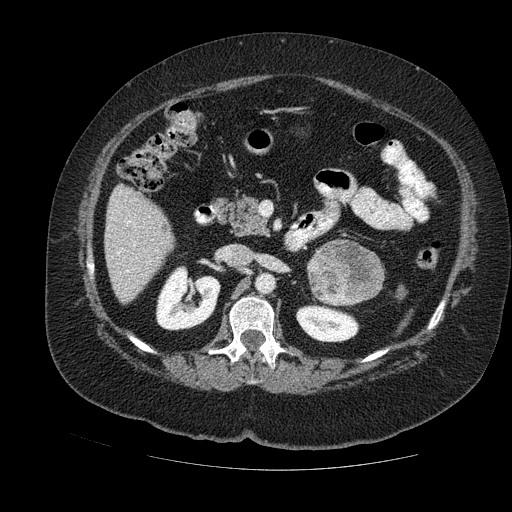
Contrast-enhanced abdominal CT, one axial slice. Slice 62 of 121 in the series (ordered by position). Soft-tissue window (W 400 / L 40 HU). 2.5 mm slice thickness. 512 × 512 image matrix, field of view 420 × 420 mm. Female patient. Case-level facts recorded for this patient, not image findings: diagnosis: adrenocortical carcinoma; tumour side: left adrenal; tumour size at pathology: 8 cm; Ki-67 index: 7 %; stage (as recorded): 2.
Annotated regions visible in this slice (semi-automatic segmentation, software-assisted and operator-edited):
- mass: bounding box <310,243,381,304> (left, top, right, bottom; pixels)